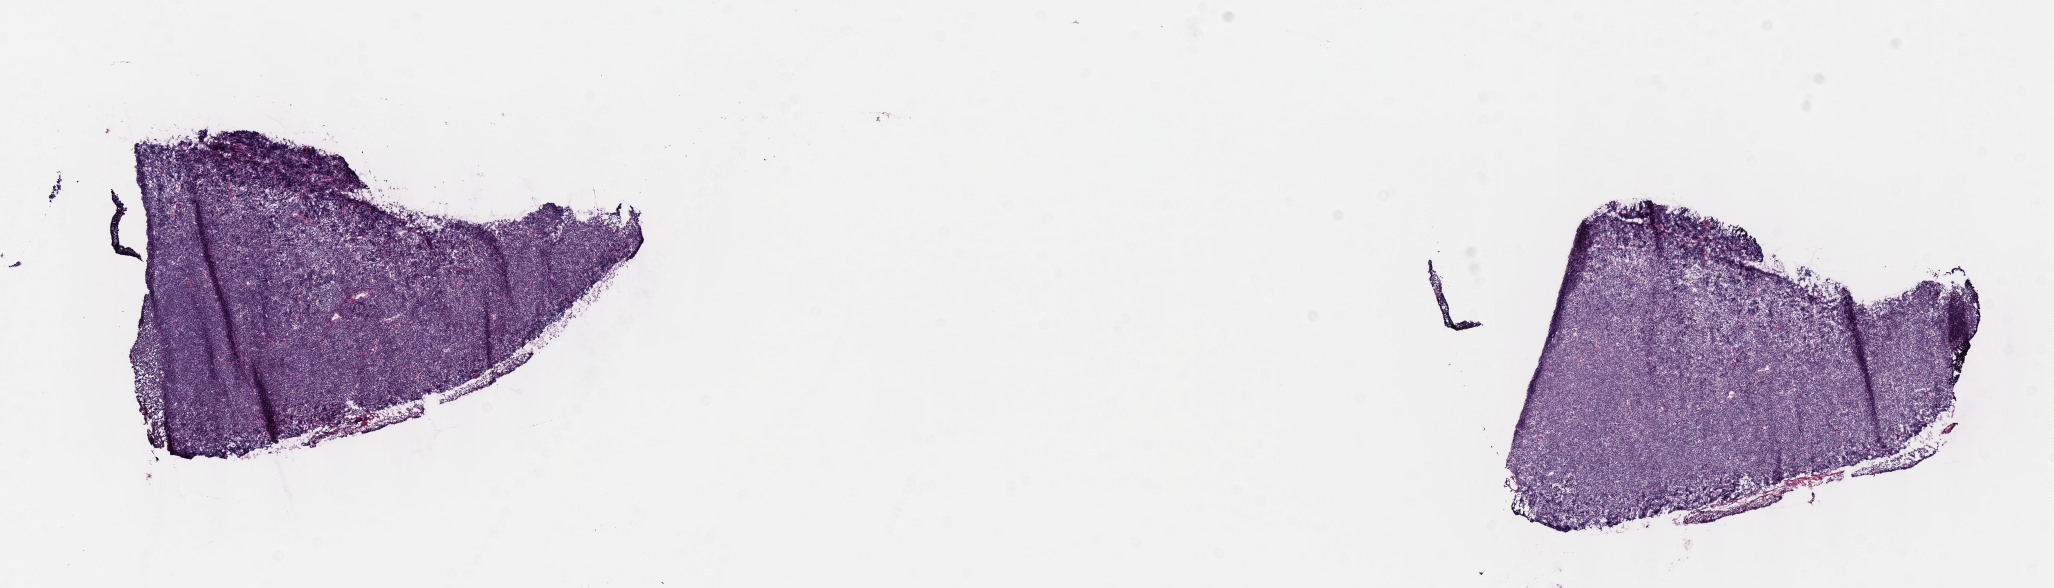
Digitized H&E-stained section, whole scanned area (about 16.6 x 4.8 mm) shown as a low-resolution overview. Frozen section. Specimen: primary tumor. Anatomic site: cranium. Female patient; age at initial diagnosis 6 years. Slide review estimates, as recorded: tumor cells 90%, tumor nuclei 90%, stromal cells 5%, necrosis 5%, normal cells 0%. Inflammatory infiltration, as recorded: lymphocyte infiltration 20%, monocyte infiltration 10%, neutrophil infiltration 10%.
Ann Arbor stage (patient): Stage IV. Histologic diagnosis: Burkitt lymphoma, NOS.